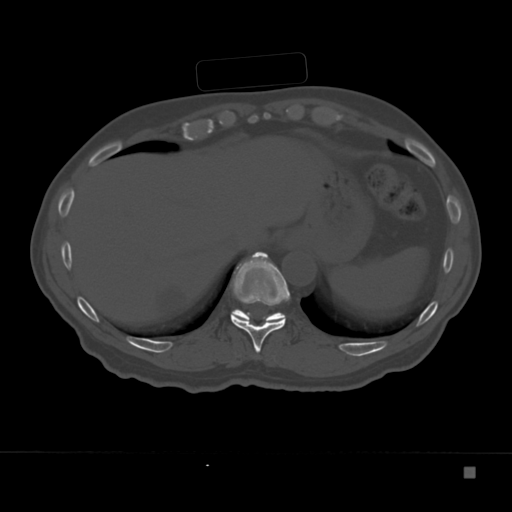
CT including the spine, one axial slice. Slice 166 of 332 in the series (ordered by position). Reconstruction kernel Br40s. Bone window (W 1800 / L 400 HU). 1.5 mm slice thickness. 512 × 512 image matrix, field of view 389 × 389 mm. Male patient, age 72 years. Case-level facts recorded for this patient, not image findings: primary cancer: skeletal.
Outlined on this slice (semi-automatic segmentation, software-assisted and operator-edited):
- T10 vertebra: bounding box [x1, y1, x2, y2] px = [230, 251, 290, 353]
- T11 vertebra: [232, 266, 285, 322]